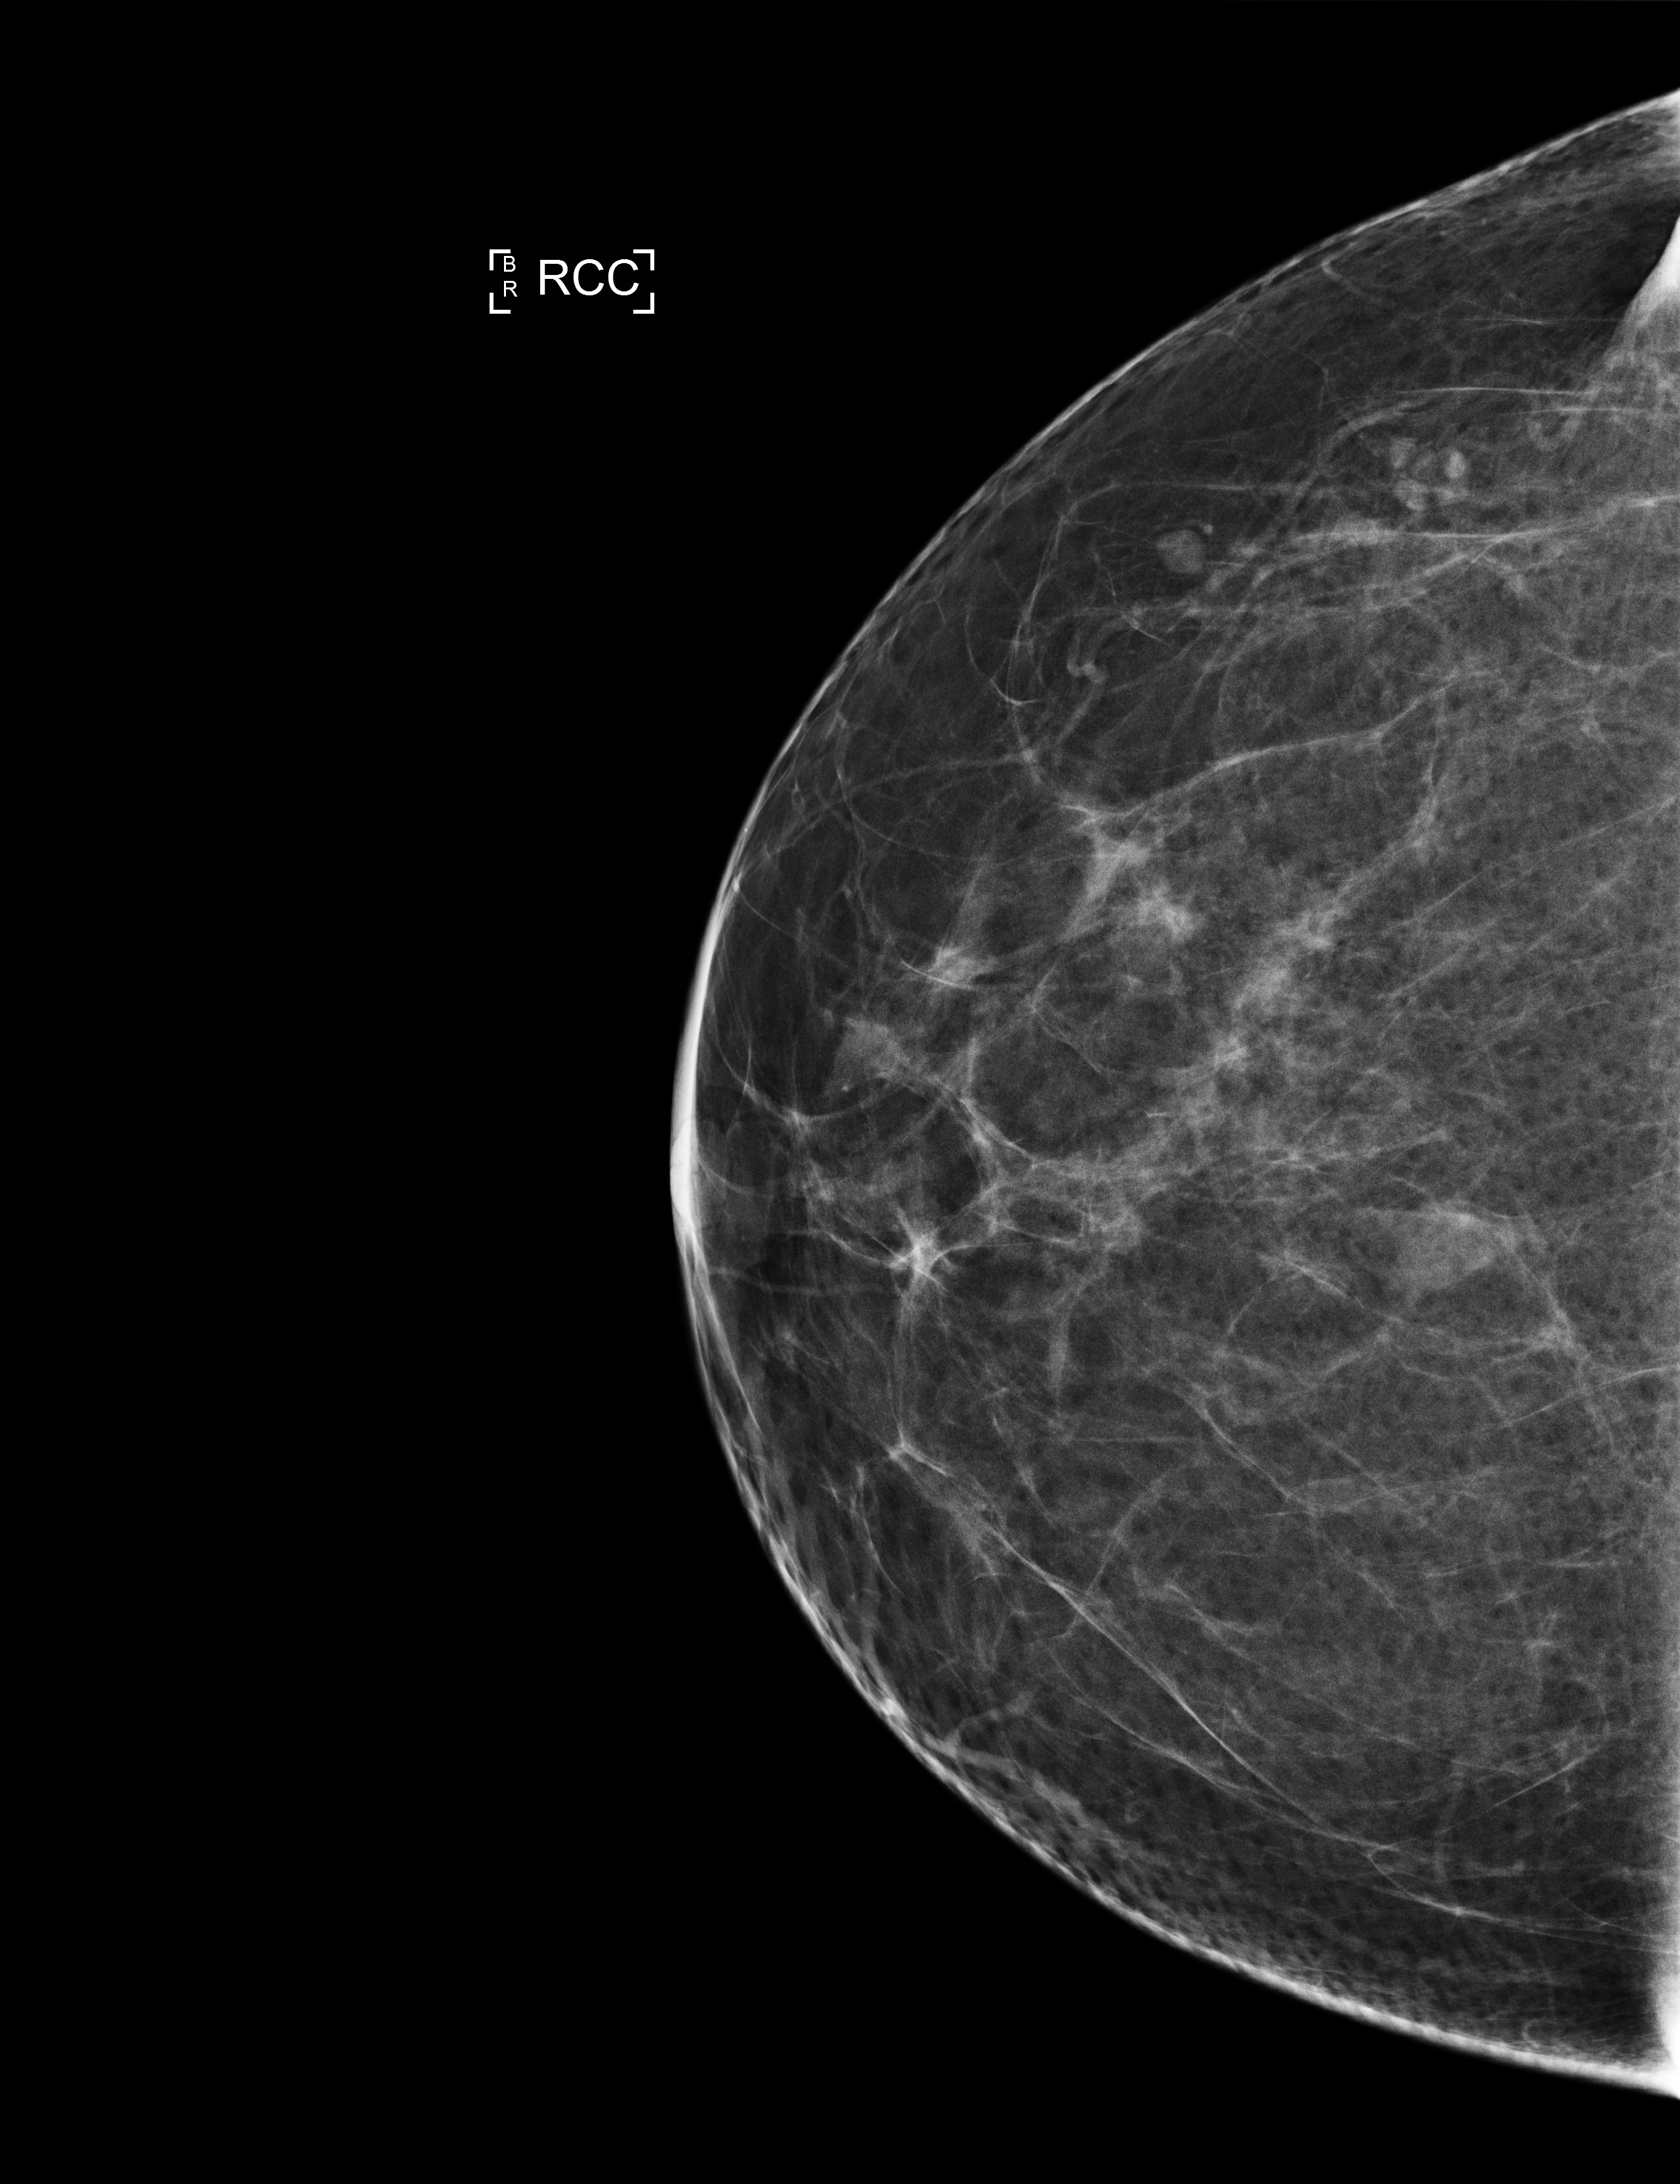
Screening examination; compressed breast thickness 98 mm; system: Selenia Dimensions. Female patient, age 44 years.
Image type: full-field digital mammogram. Breast: right. Projection: CC view.